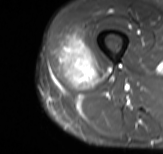
MRI of an extremity soft-tissue mass, one axial slice. Slice 25 of 61 in the series (ordered by position). STIR. MR volume resampled by the dataset authors to the PET/CT grid (not the native acquisition matrix). 163 × 154 image matrix, field of view 159 × 150 mm. Male patient. Case-level facts recorded for this patient, not image findings: histological type: poorly differentiated synovial sarcoma; grade: high; site of the primary tumour: right buttock.
Structures marked on this image (expert contour drawn on MRI and transferred to this co-registered scan by the dataset authors):
- gross tumour volume including surrounding oedema: bounding box [x1, y1, x2, y2] px = [57, 34, 111, 90]
- gross tumour volume (mass): [59, 36, 97, 86]